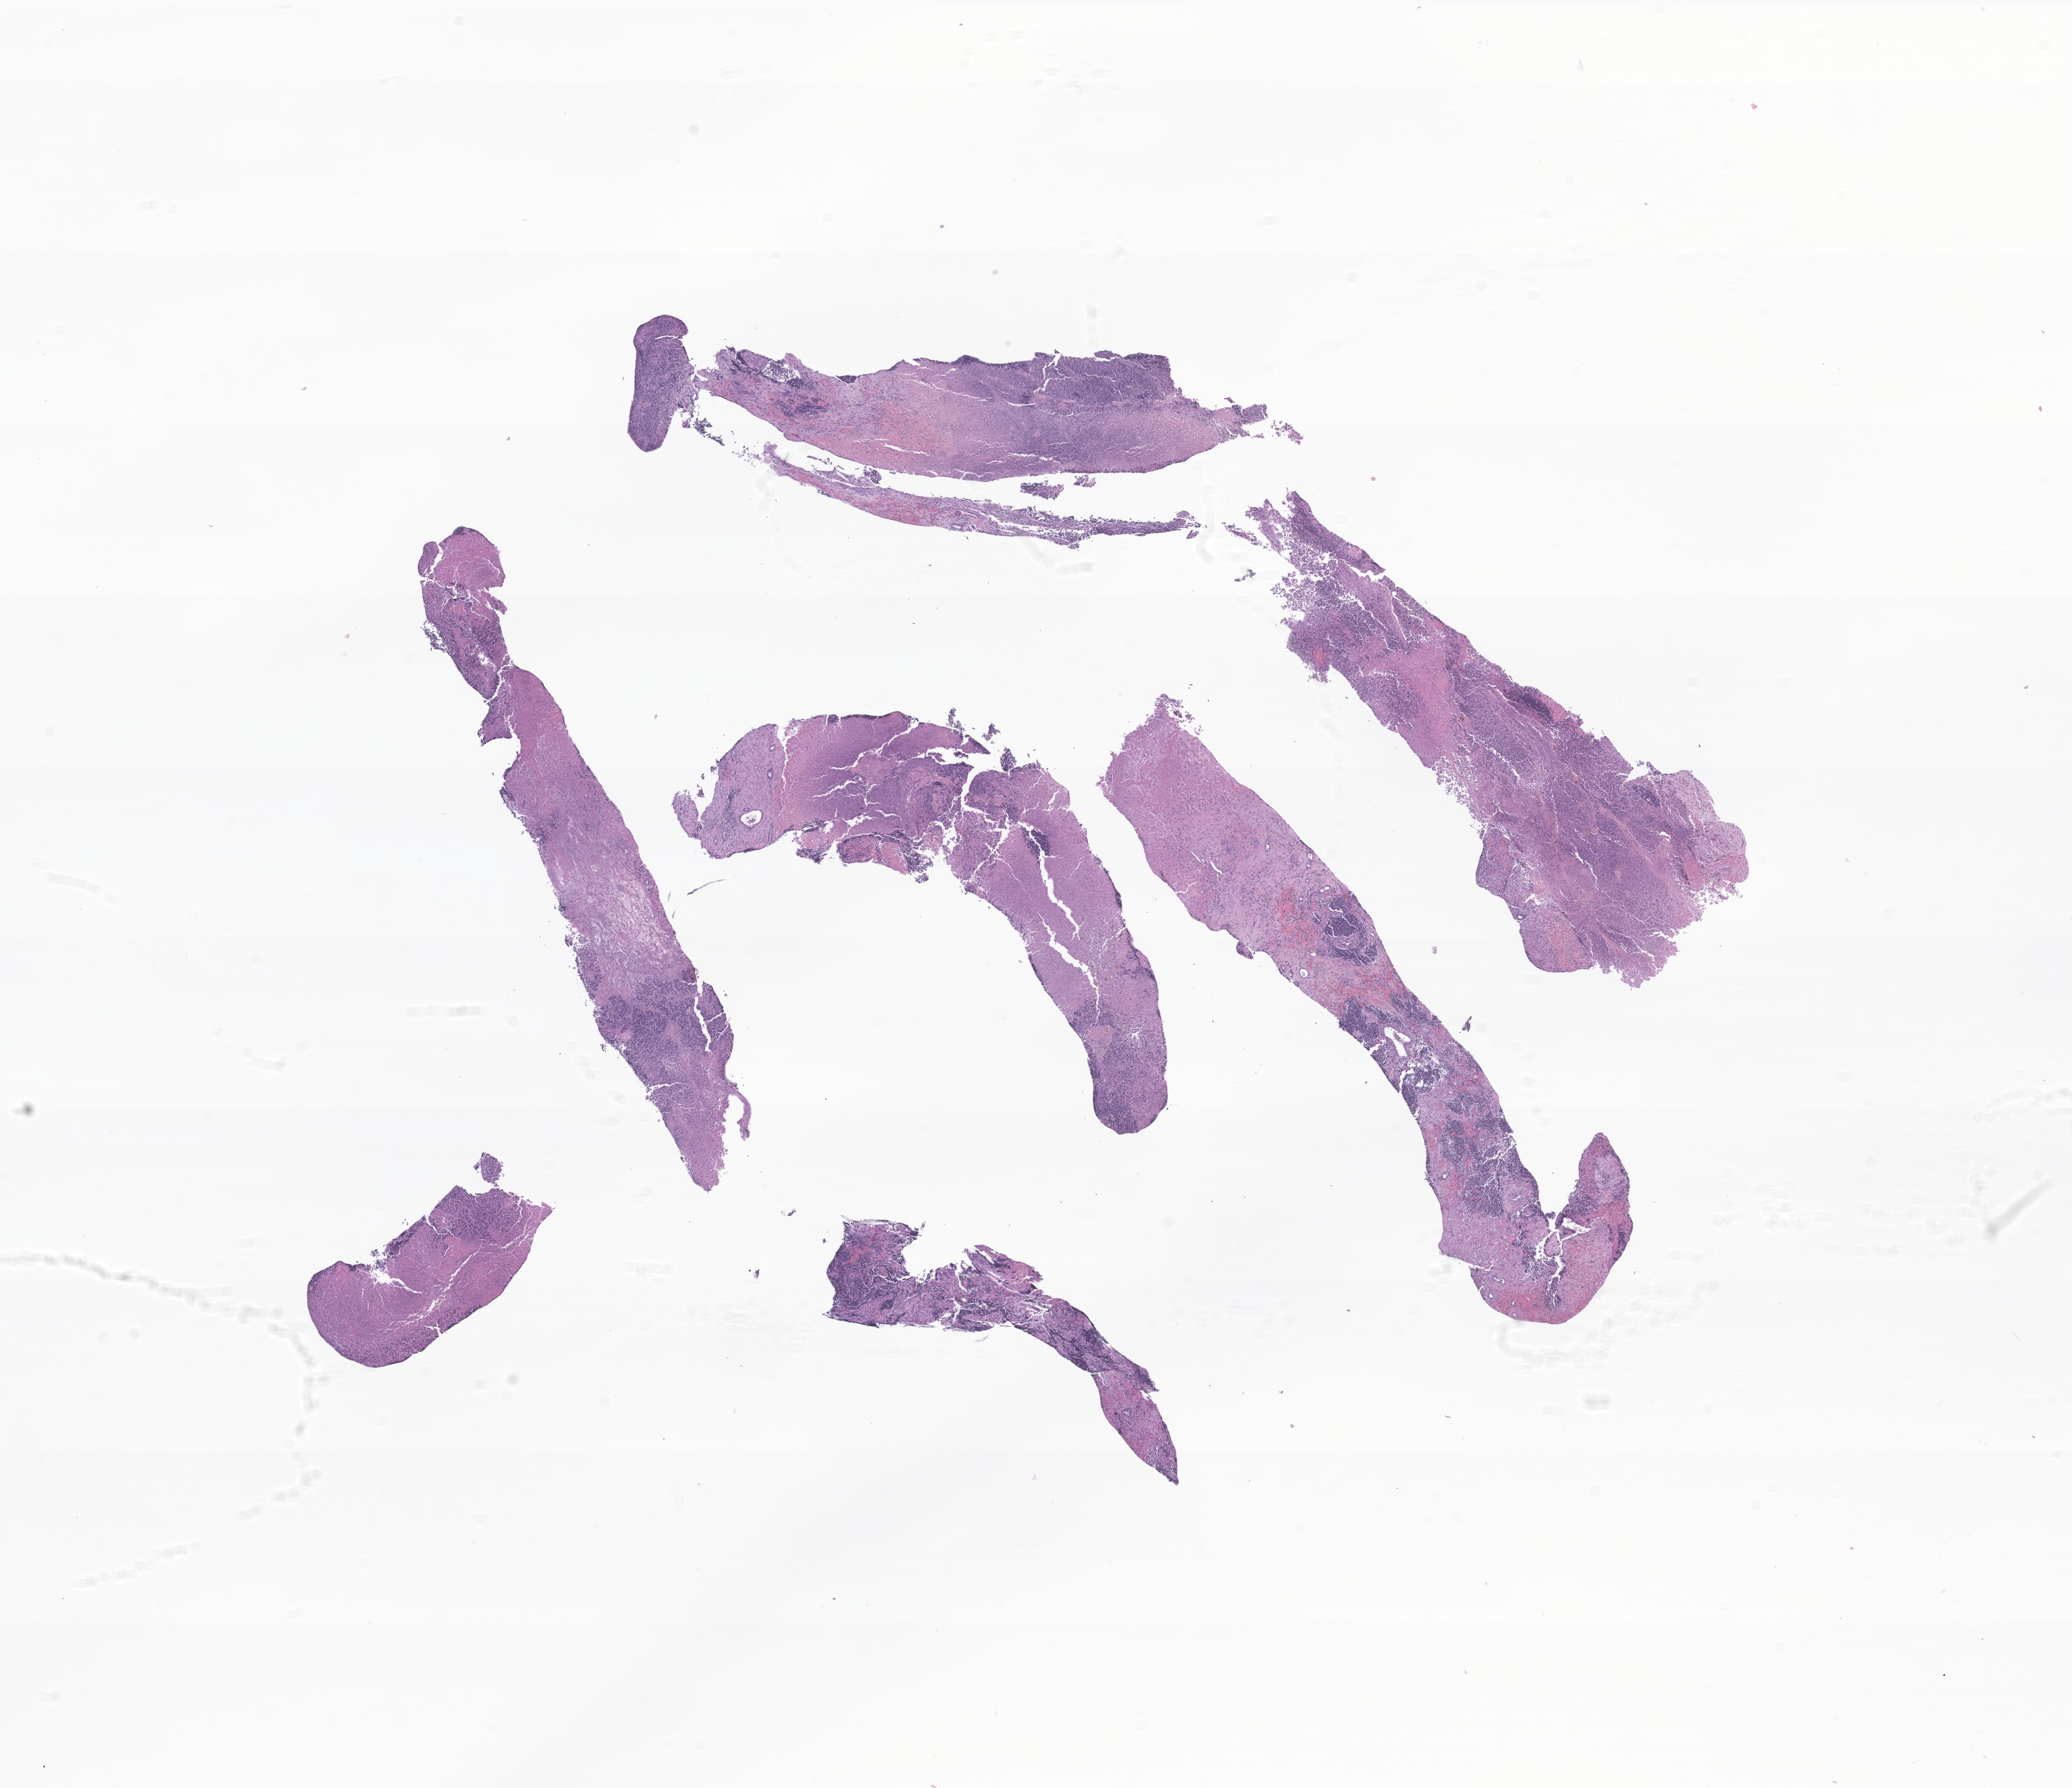
Digitized hematoxylin and eosin (H&E)-stained section of tumor tissue from the adrenal gland, whole scanned area (about 12.9 x 11.2 mm) shown as a low-resolution overview; formalin-fixed paraffin-embedded section. Patient: male, age 749 days.
Diagnosis (ICD-O-3 morphology term): Neuroblastoma, NOS.